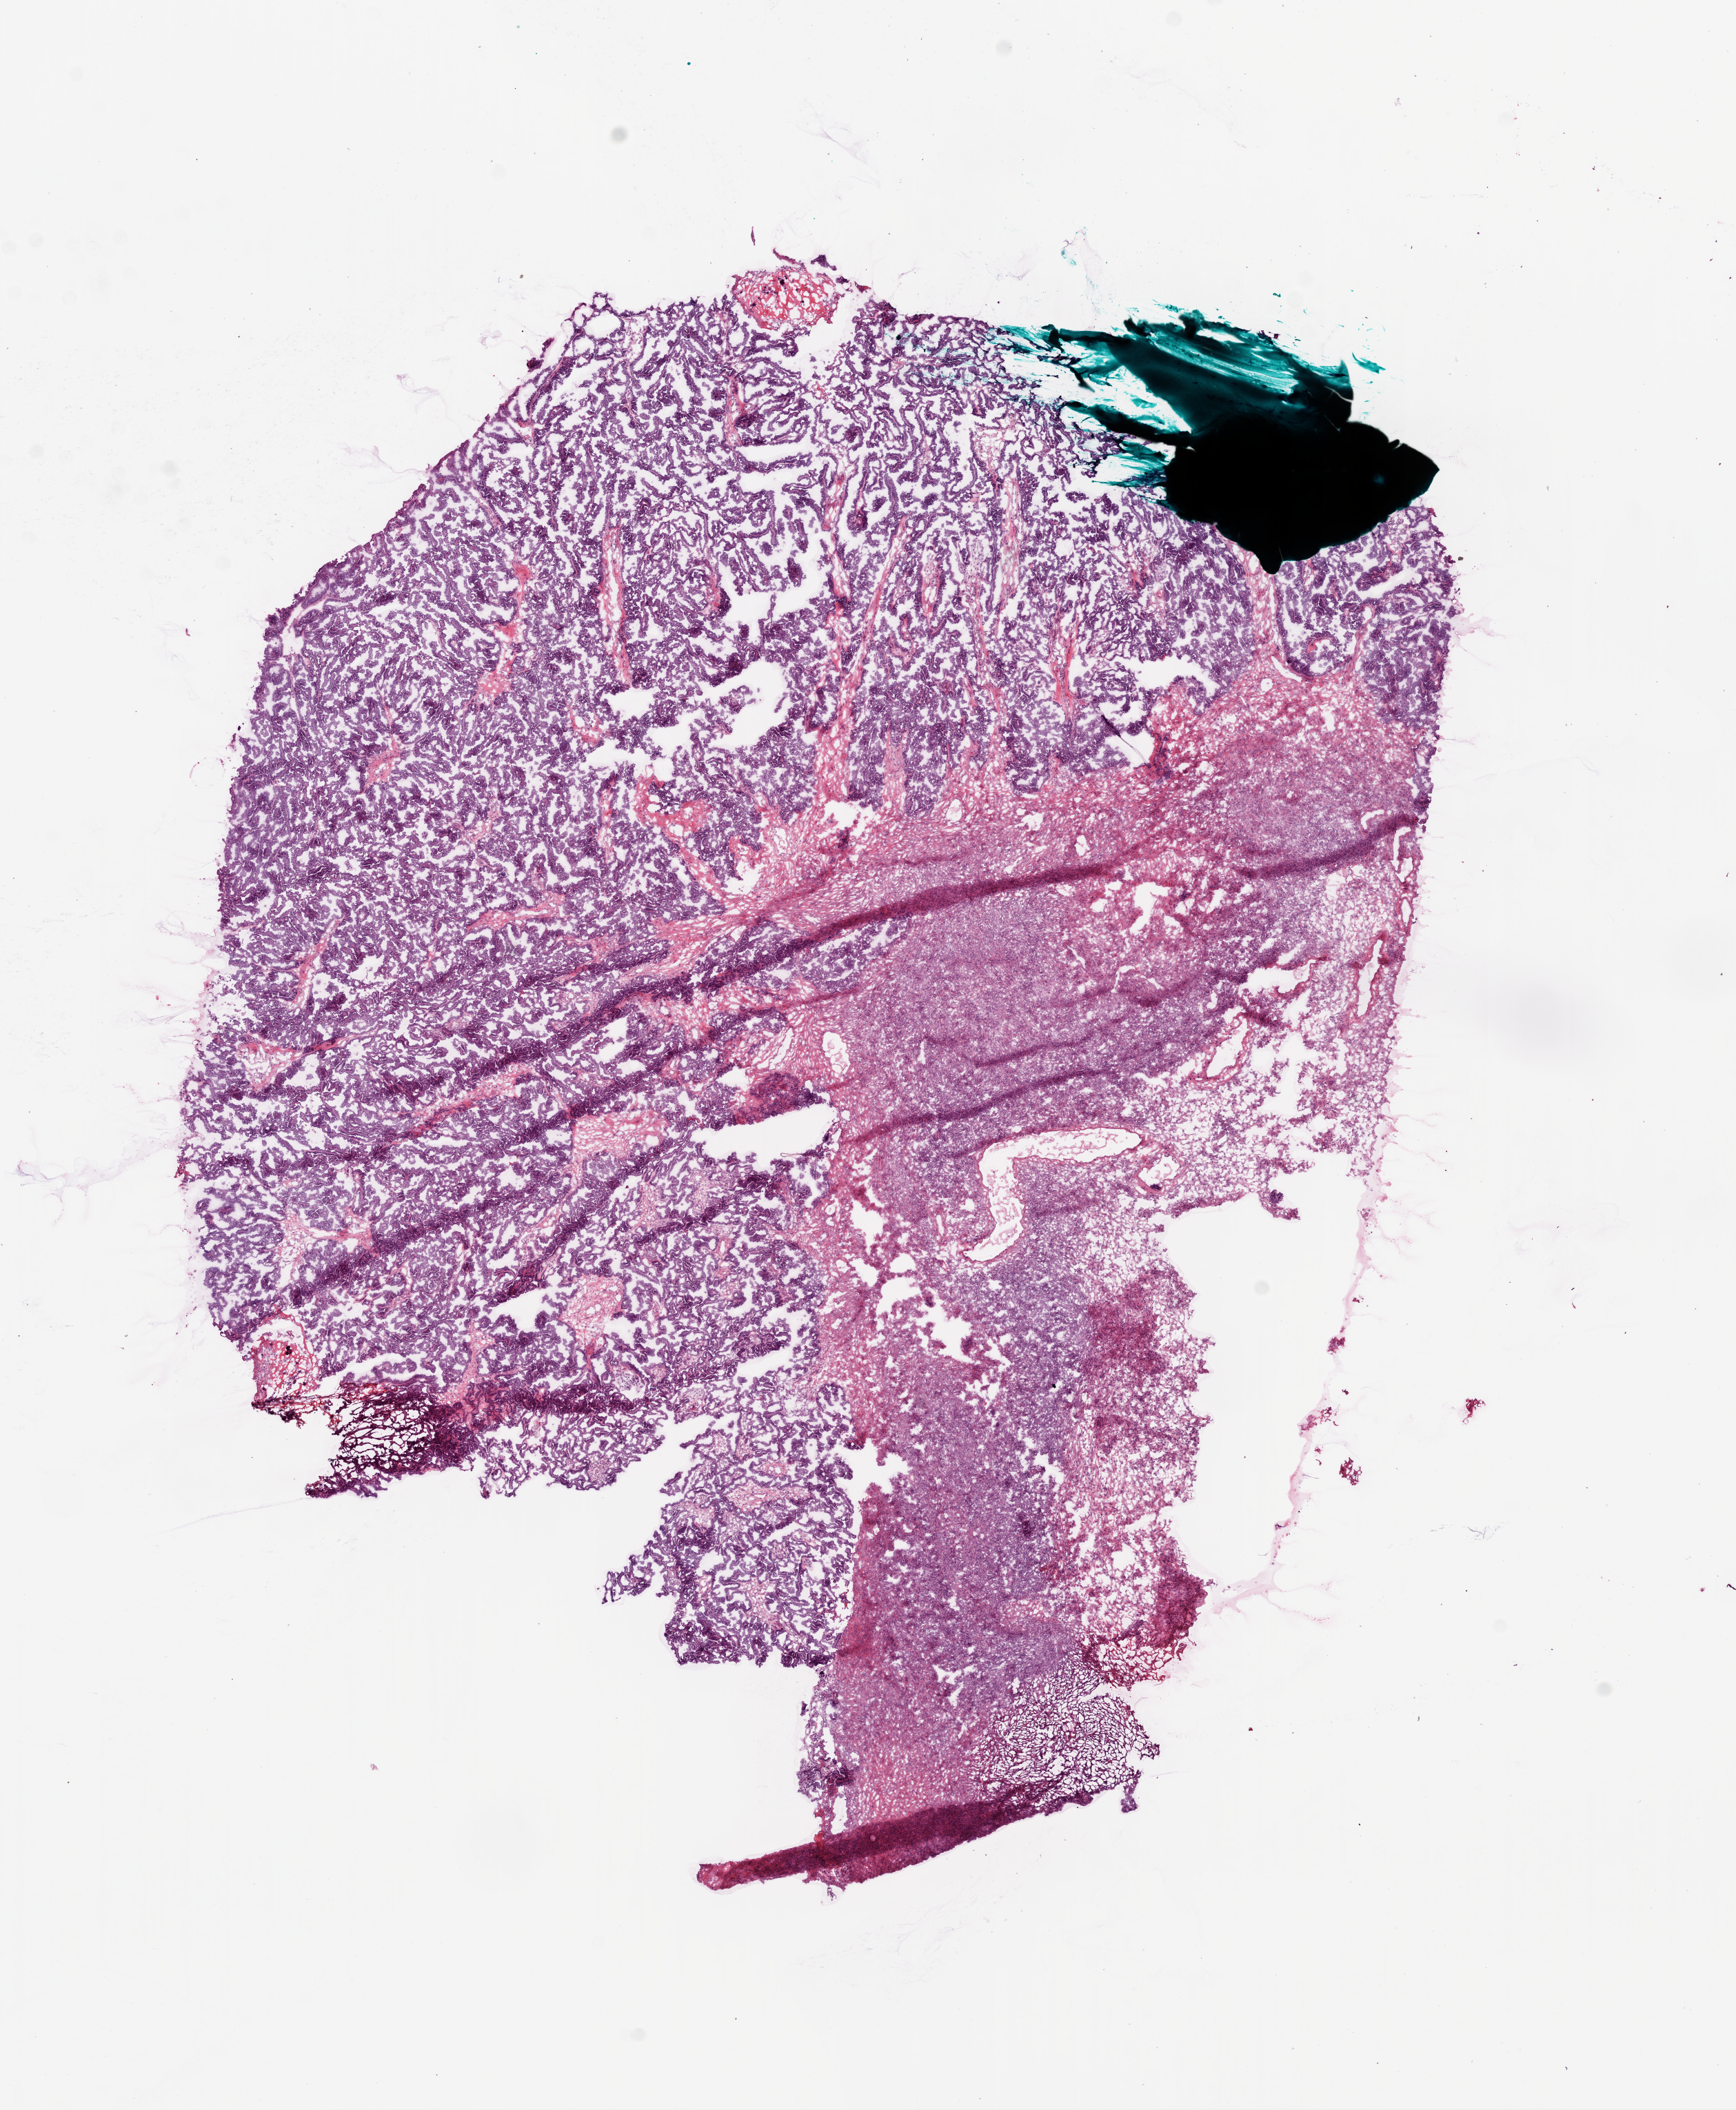
H&E-stained whole-slide image, low-resolution overview of the scanned area, about 10.2 x 12.3 mm; frozen section; primary tumour sample from the ovary. Female, age 65 years at initial diagnosis. Histologic grade: G2 (moderately differentiated). Slide review estimates, as recorded: tumour cells 90%, tumour nuclei 95%, normal cells 5%, stromal cells 5%, necrosis 0%.
FIGO stage: IIIC. Diagnosis: Serous cystadenocarcinoma, NOS.